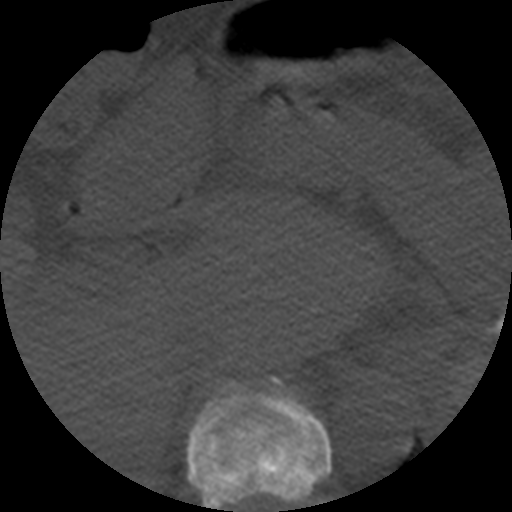
CT including the spine, one axial slice. Slice 257 of 508 in the series (ordered by position). 120 kVp. Bone window (W 1800 / L 400 HU). 1.25 mm slice thickness. 512 × 512 image matrix. Patient age 57 years. Case-level facts recorded for this patient, not image findings: primary cancer: prostate.
Structures marked on this image (semi-automatically segmented with operator editing):
- T10 vertebra: bounding box <187,378,331,512> (left, top, right, bottom; pixels)